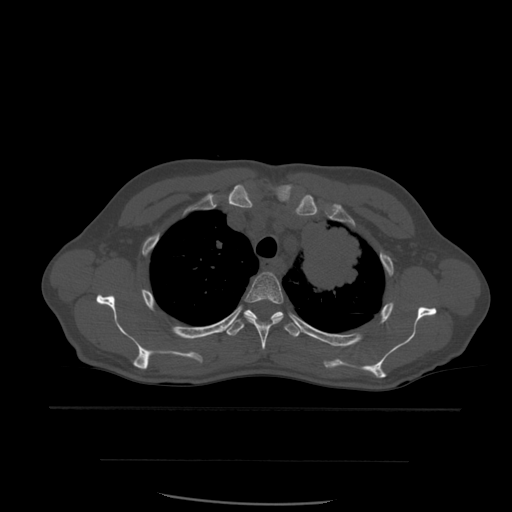
CT including the spine, one axial slice; slice 437 of 574 in the series (ordered by position); bone window (W 1800 / L 400 HU); 1.25 mm slice thickness; 512 × 512 image matrix, field of view 392 × 392 mm. Patient age 48 years. Case-level facts recorded for this patient, not image findings: primary cancer: lung; vertebrae with lytic lesions (as recorded): T11.
Annotated regions visible in this slice (semi-automatic segmentation, software-assisted and operator-edited):
- T3 vertebra: bounding box (x1, y1, x2, y2) in pixels: (244, 272, 284, 350)
- T4 vertebra: (225, 310, 303, 338)